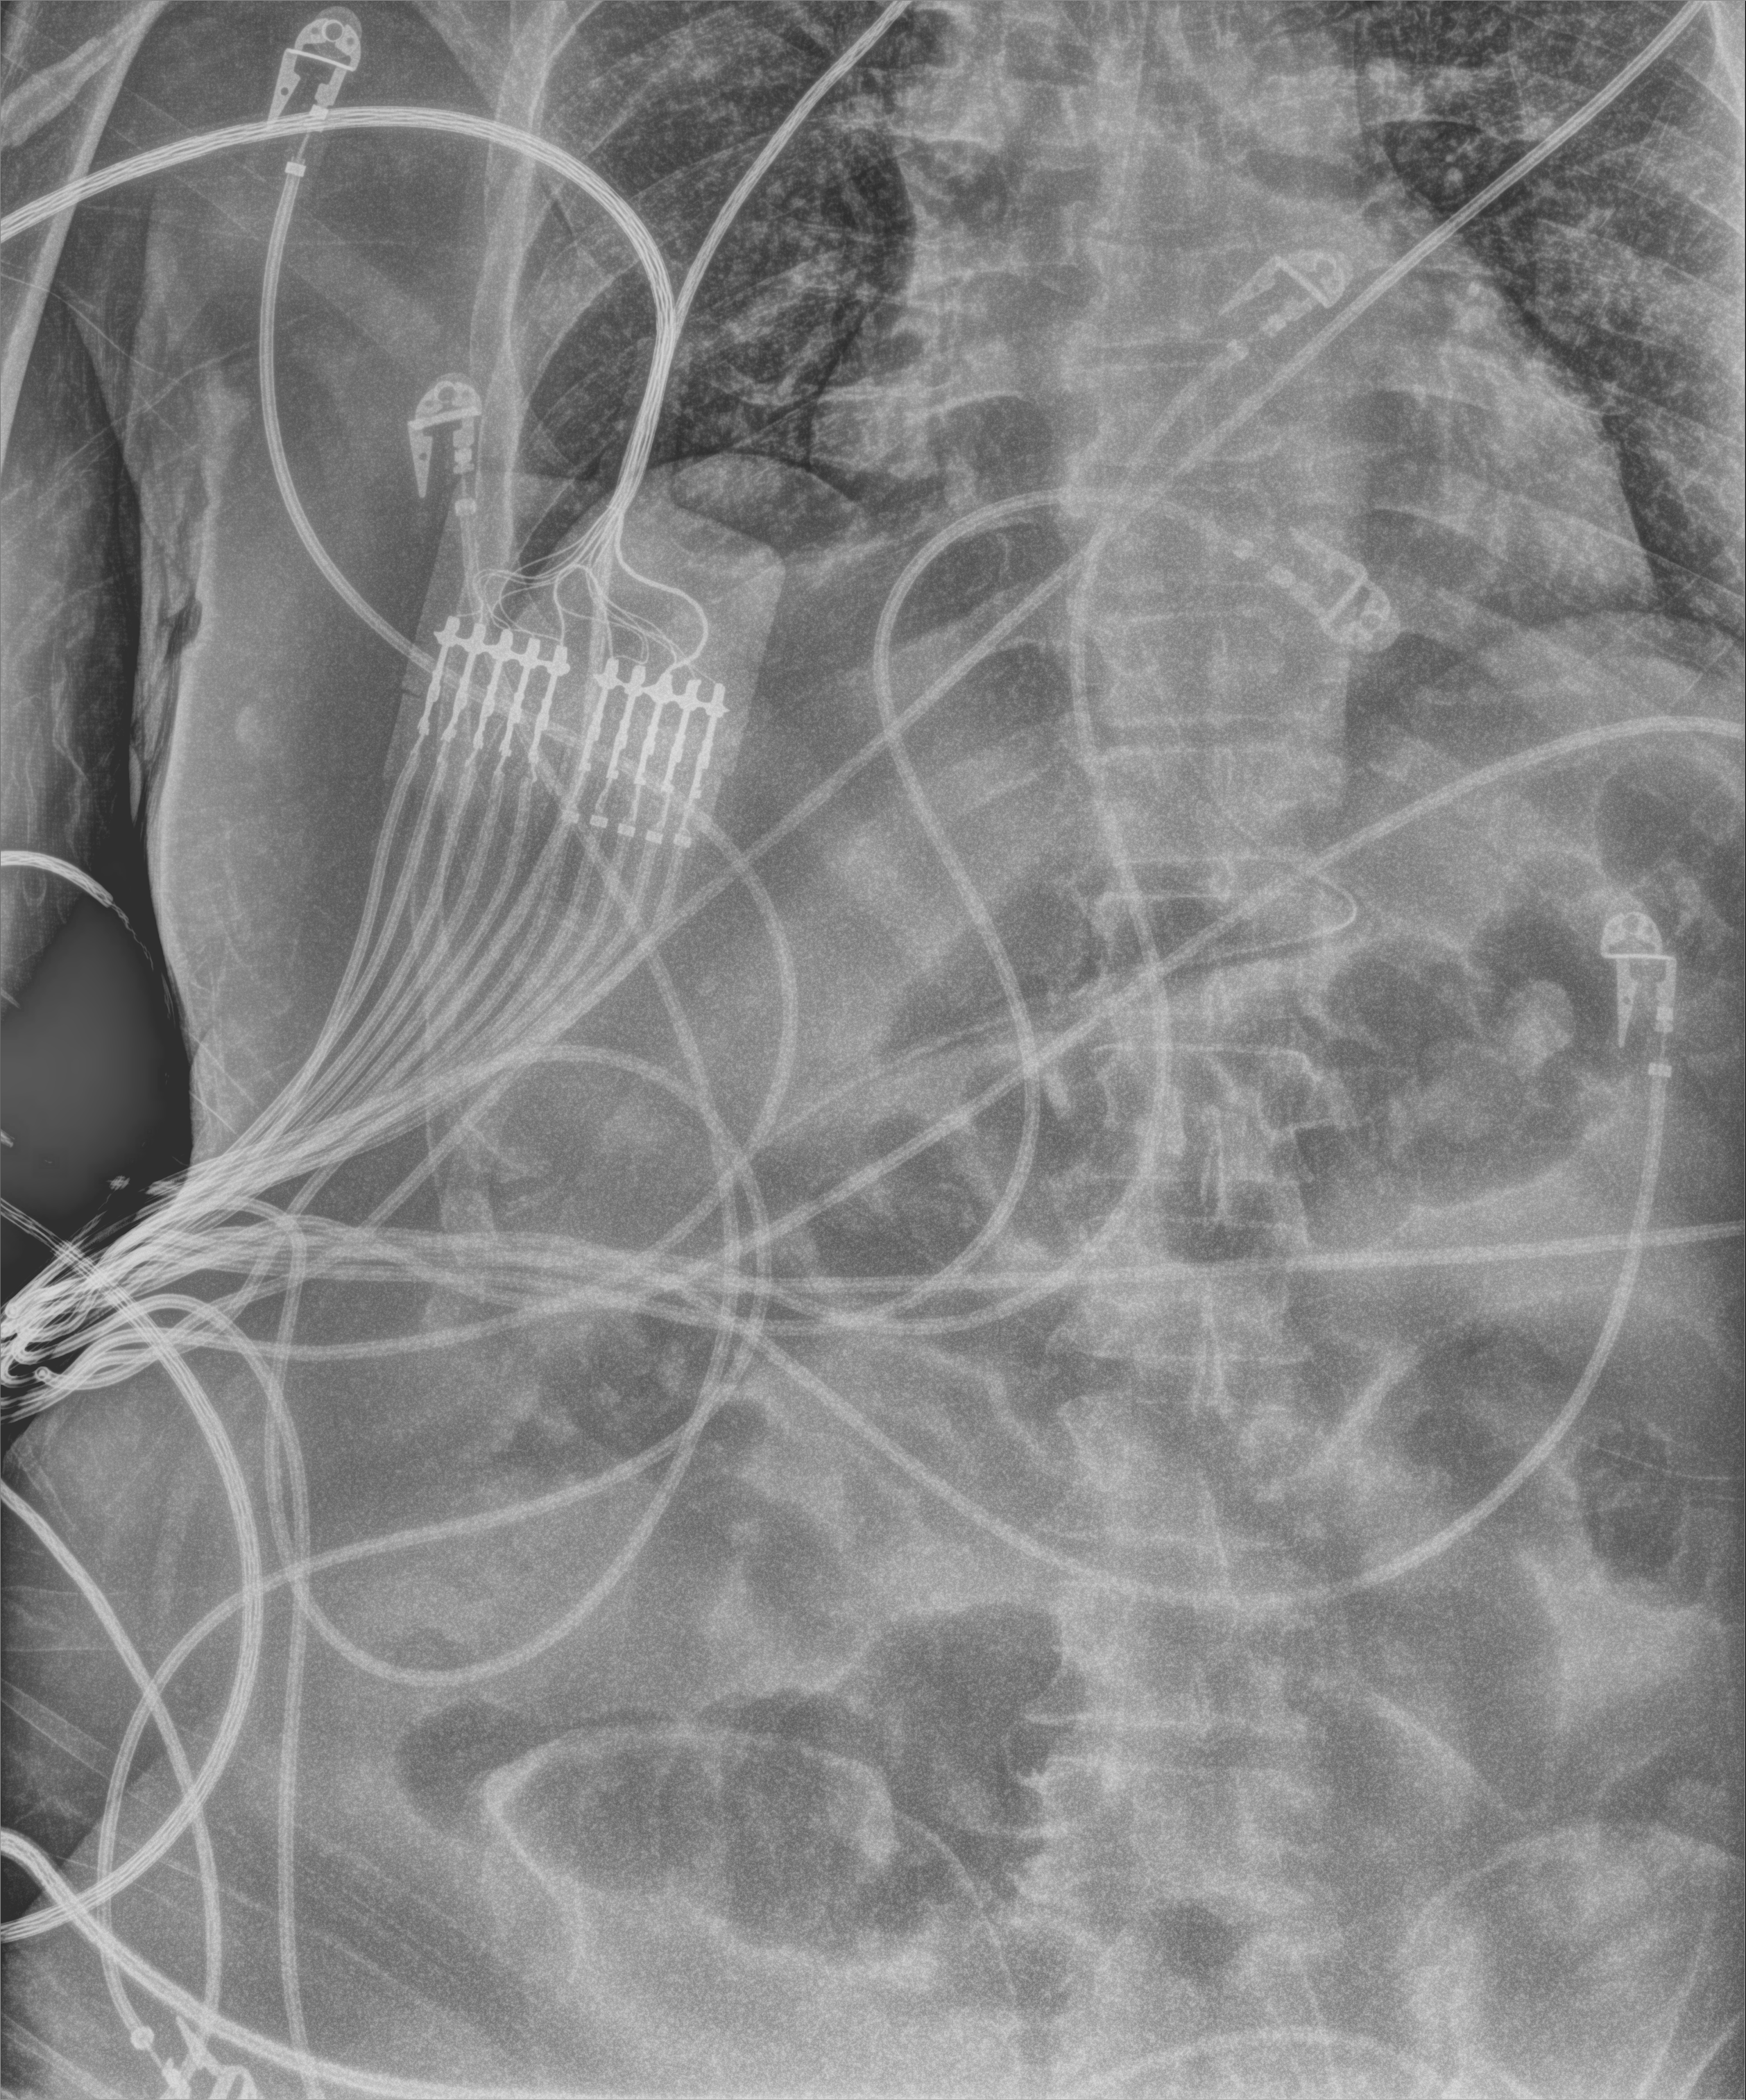
Chest X-ray (portable), anteroposterior (AP) projection. Patient hospitalised with COVID-19, aged 18–59 years.
From the hospital-stay record, not from the radiograph (when in the stay this image was taken is not recorded): mechanically ventilated during this hospital stay: yes; admitted to intensive care during this hospital stay: yes.